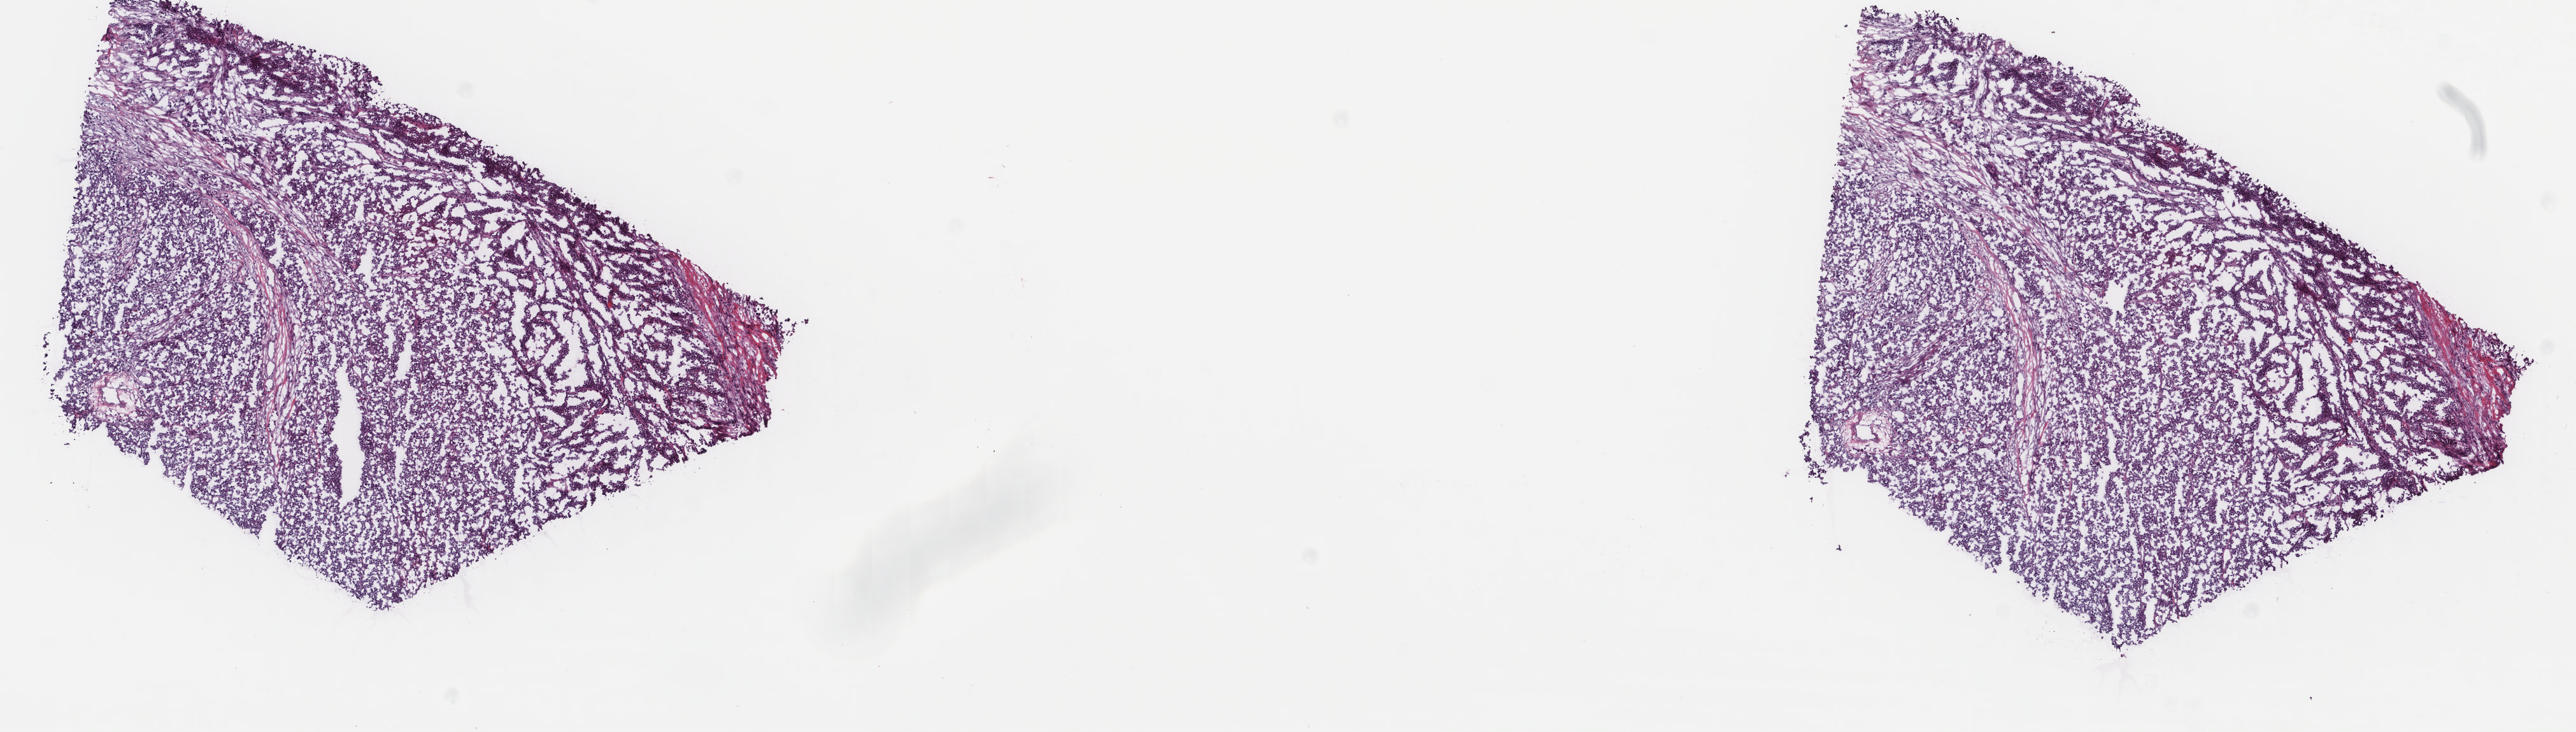
Whole-slide histology image, Hematoxylin and eosin (H&E) stained, whole scanned area (about 16.1 x 4.6 mm) shown as a low-resolution overview; frozen section from the top of the tissue portion; metastatic tumour sample, sampled site: lymph node. Male, age 42 years at initial diagnosis. Pathologist review of this section (percent, as recorded): tumour cells 85%, tumour nuclei 85%, normal cells 0%, stromal cells 15%, necrosis 0%. Inflammatory infiltration, as recorded: lymphocyte infiltration 5%, monocyte infiltration 0%, neutrophil infiltration 0%.
This section: metastatic tumour tissue. Patient diagnosis: Malignant melanoma, NOS.